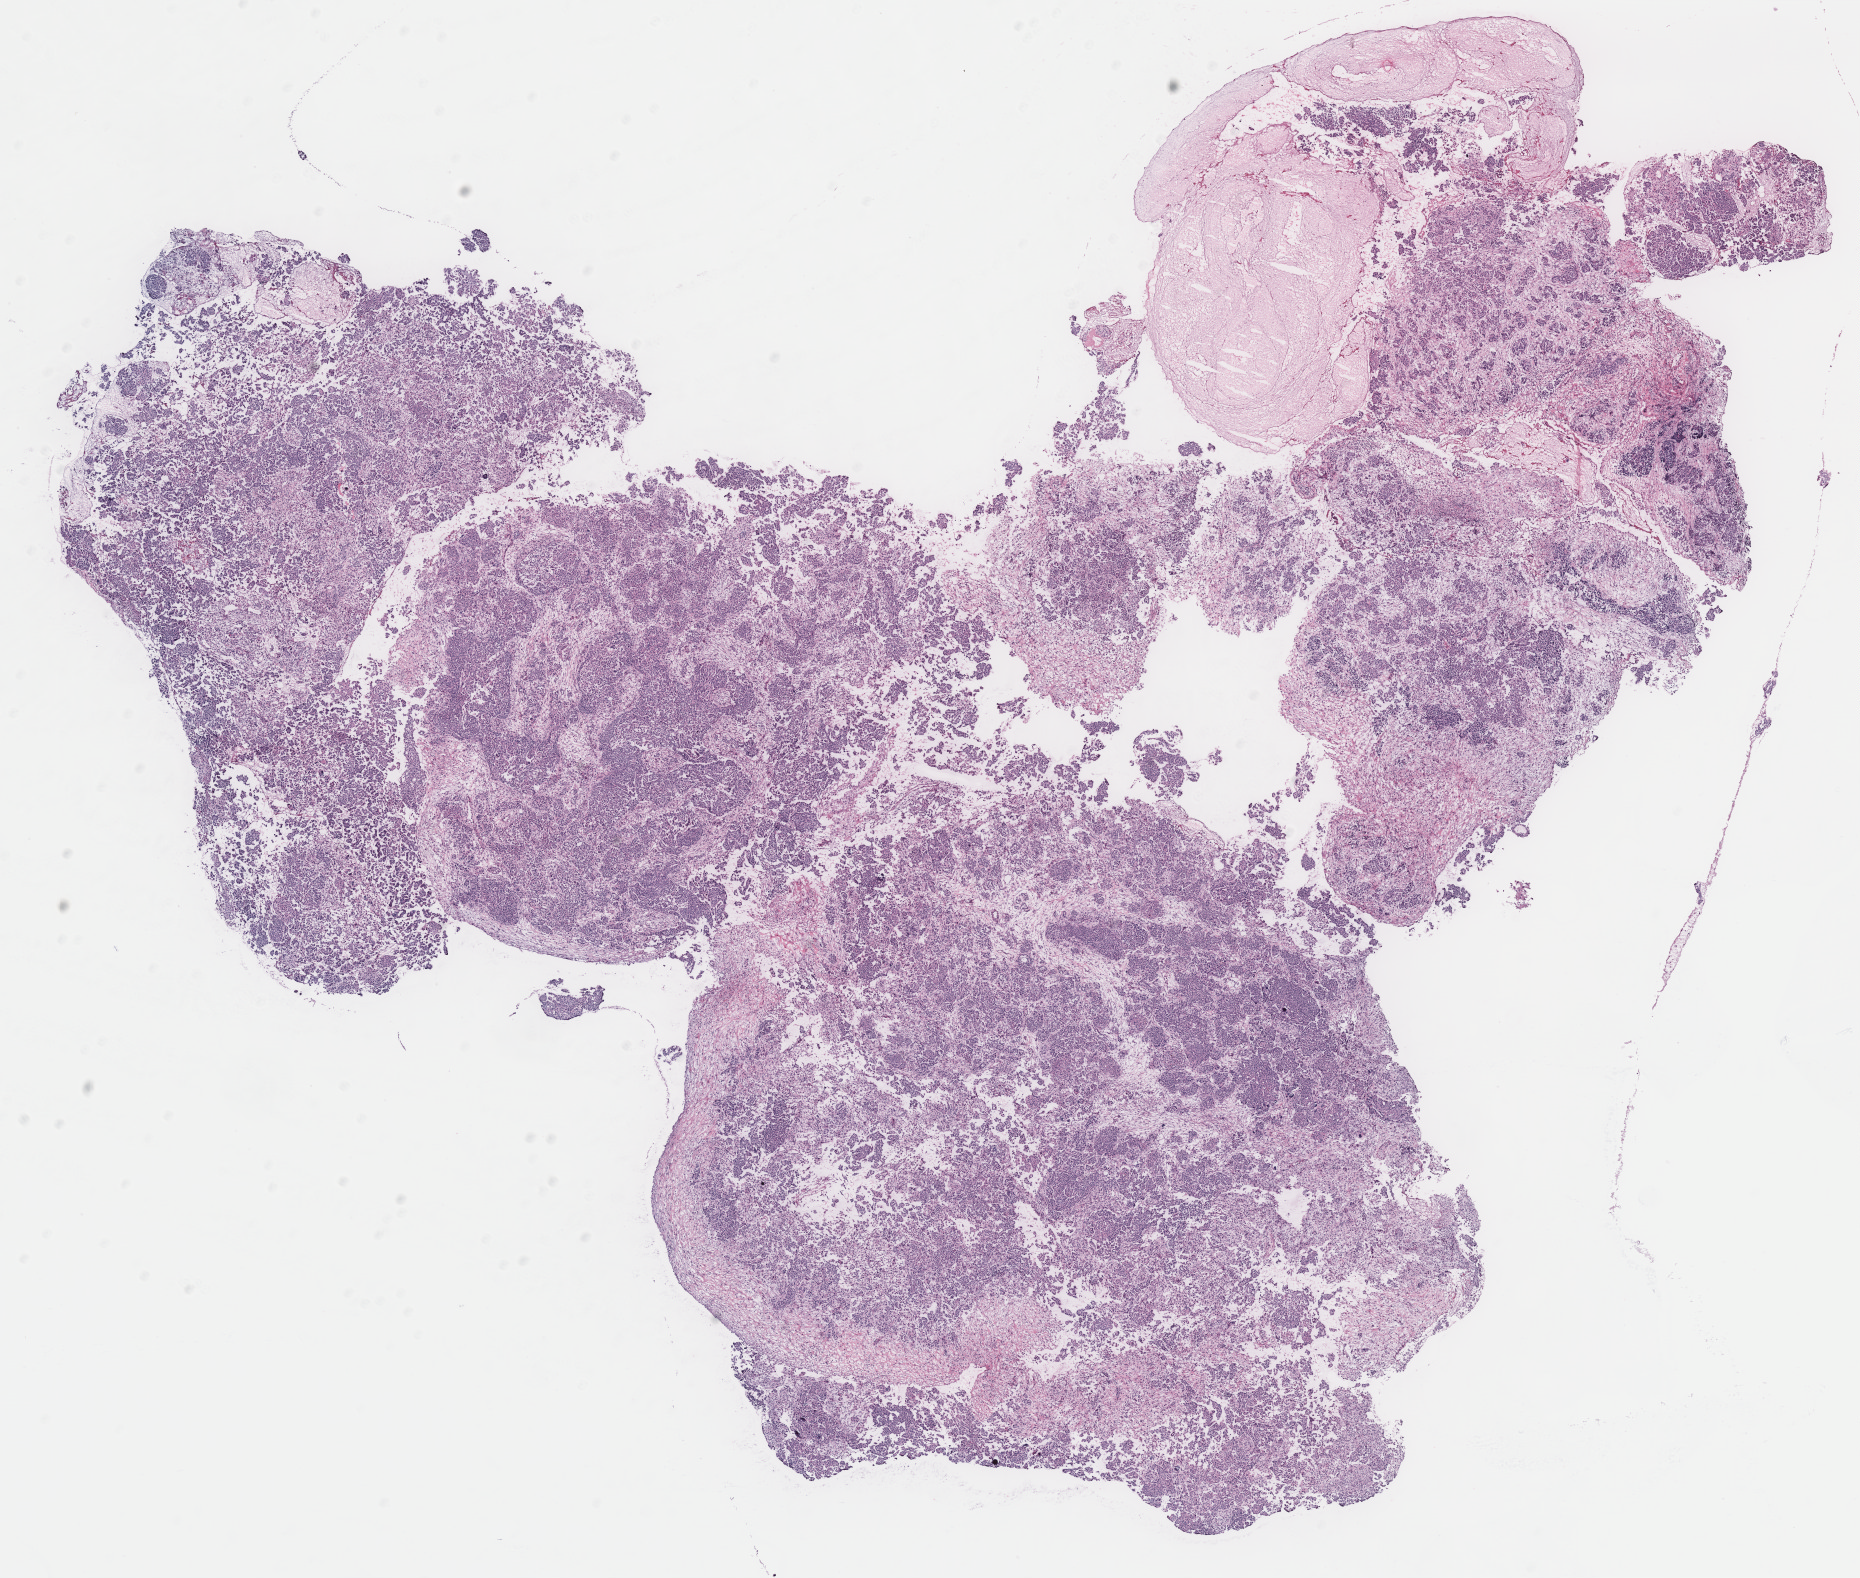
Whole-slide histology image, H&E, low-resolution overview of the scanned area, about 14.9 x 12.6 mm; tumour tissue sample, ovary. Female, 51 y/o.
Histologic diagnosis: Serous adenocarcinoma, NOS (peritoneum, NOS). Primary tumour site (as recorded): peritoneum.